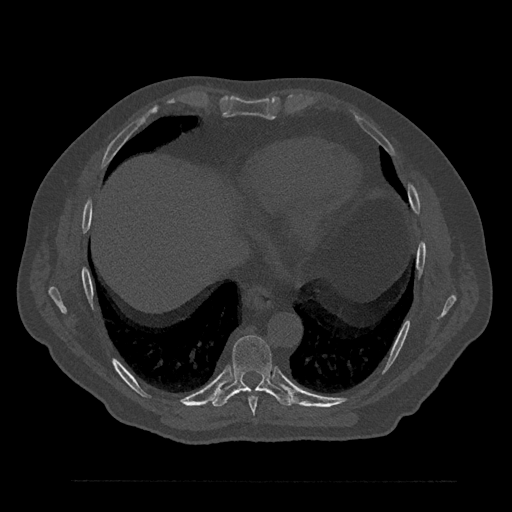
CT including the spine, one axial slice. Slice 422 of 797 in the series (ordered by position). Reconstruction kernel Br40s/3. 120 kVp. Bone window (W 1800 / L 400 HU). 512 × 512 image matrix, field of view 430 × 430 mm. Patient: male, 61 years. From the clinical record (not read from this slice): primary cancer: prostate.
Structures marked on this image (semi-automatically segmented with operator editing):
- T8 vertebra: box from (x=240, y=391) to (x=258, y=415) px
- T9 vertebra: (x=212, y=335)–(x=294, y=407)